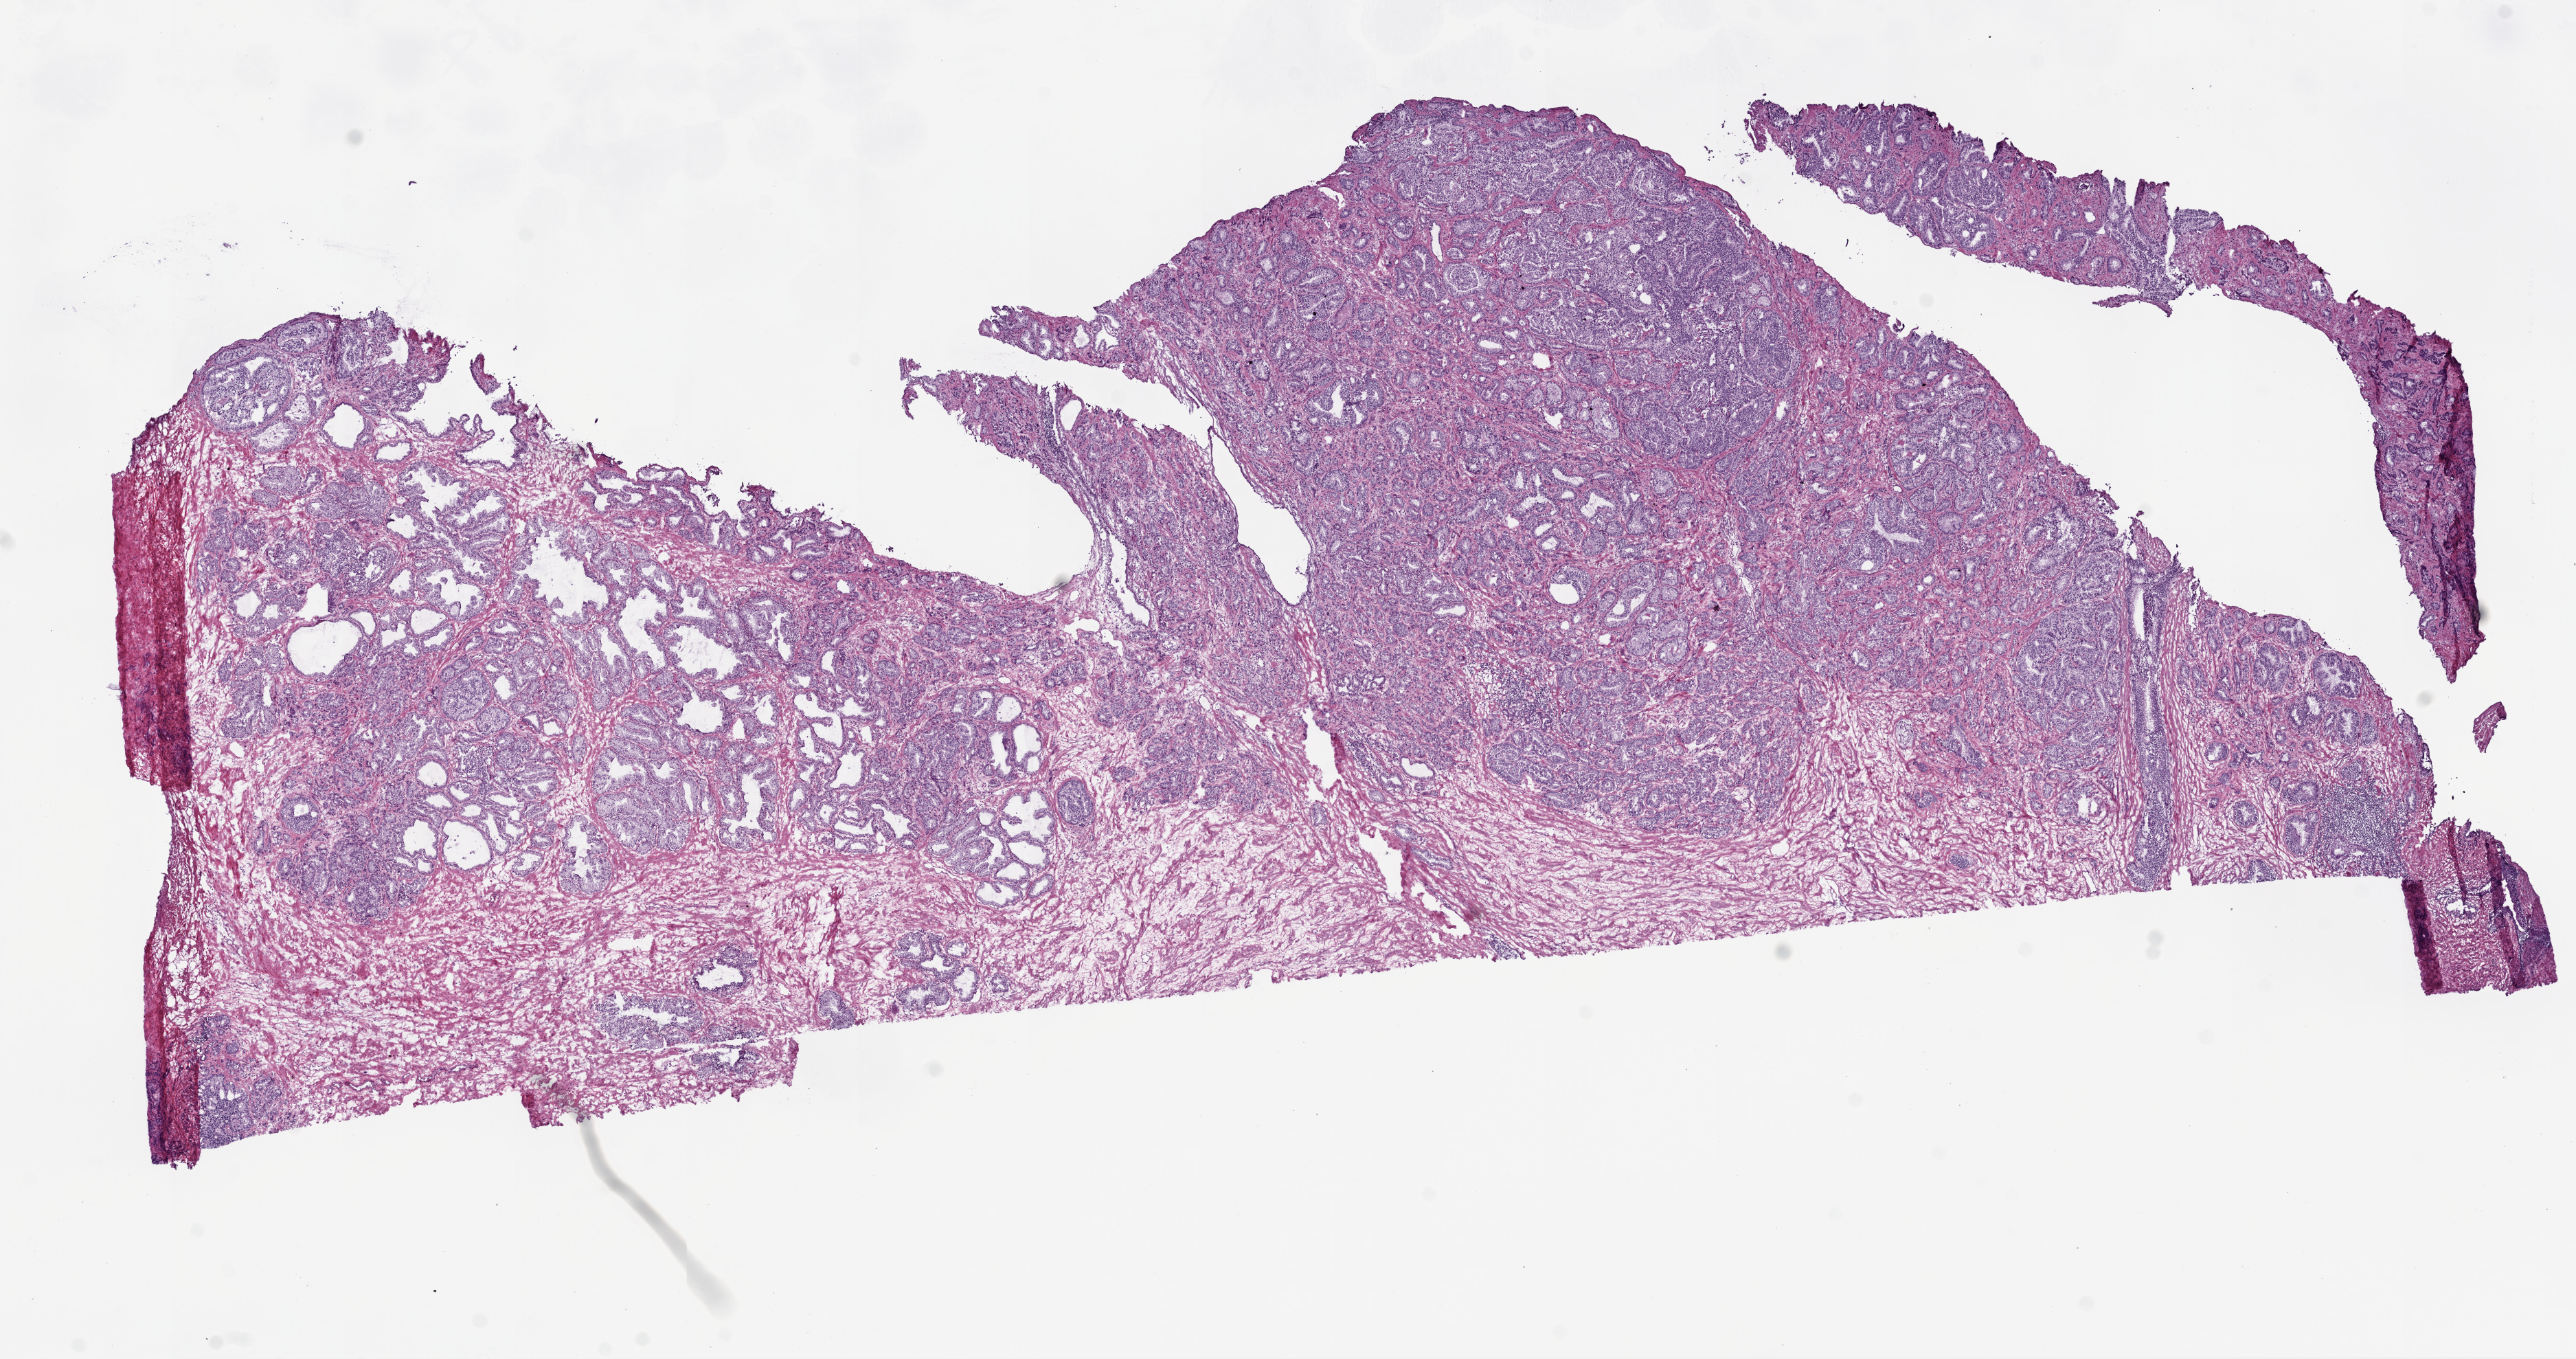
H&E whole-slide image, shown as a low-resolution overview of the whole scanned area (about 15.0 x 7.9 mm); frozen section; primary tumour sample from the prostate. Male, age 60 years at initial diagnosis. Gleason score: 7 (3+4). Pathologist review of this section (percent, as recorded): tumour cells 60%, tumour nuclei 65%, normal cells 15%, stromal cells 25%, necrosis 0%. Infiltration values recorded for this section: lymphocyte infiltration 3%, monocyte infiltration 0%, neutrophil infiltration 0%.
Laterality: right. Pathologic diagnosis: Acinar cell carcinoma.